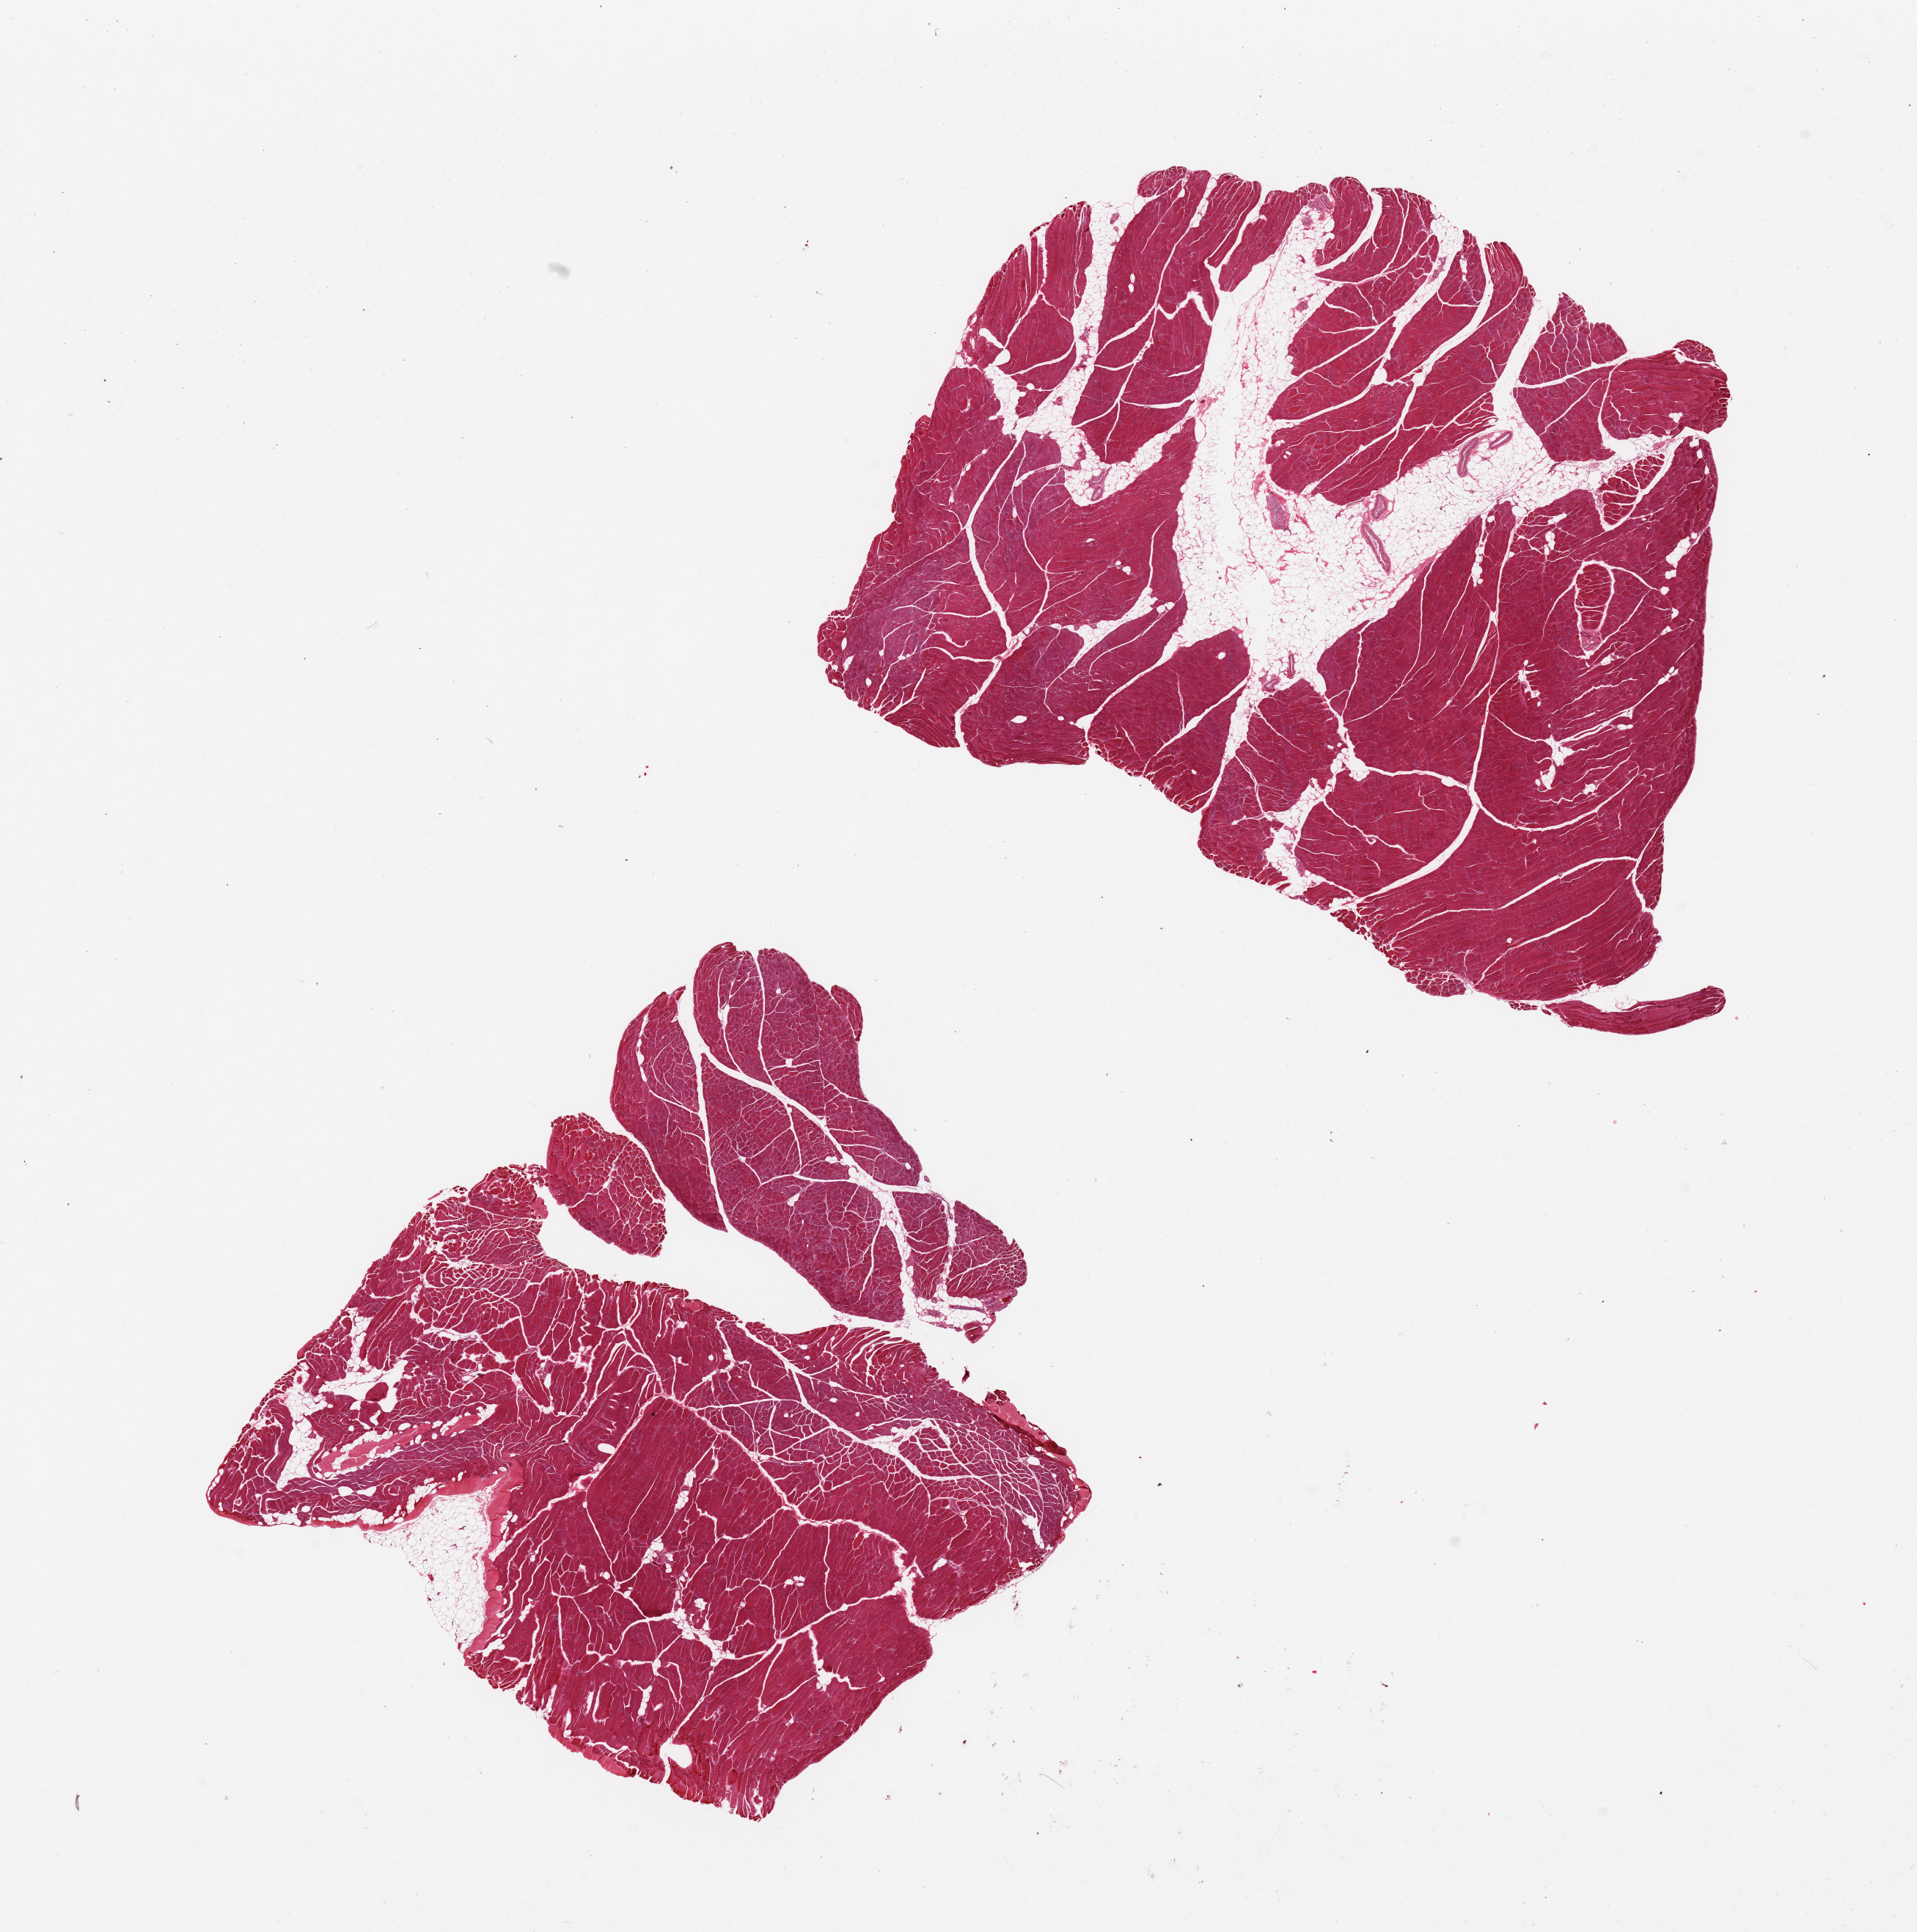
Haematoxylin and eosin whole-slide image — low-resolution overview of the scanned area, about 20.7 x 20.8 mm, PAXgene-fixed paraffin-embedded (PFPE) section, sampled site (target tissue): skeletal muscle, donor tissue sample. Donor: female.
* reviewer comment on this tissue sample: 2 pieces 20% interstial fat